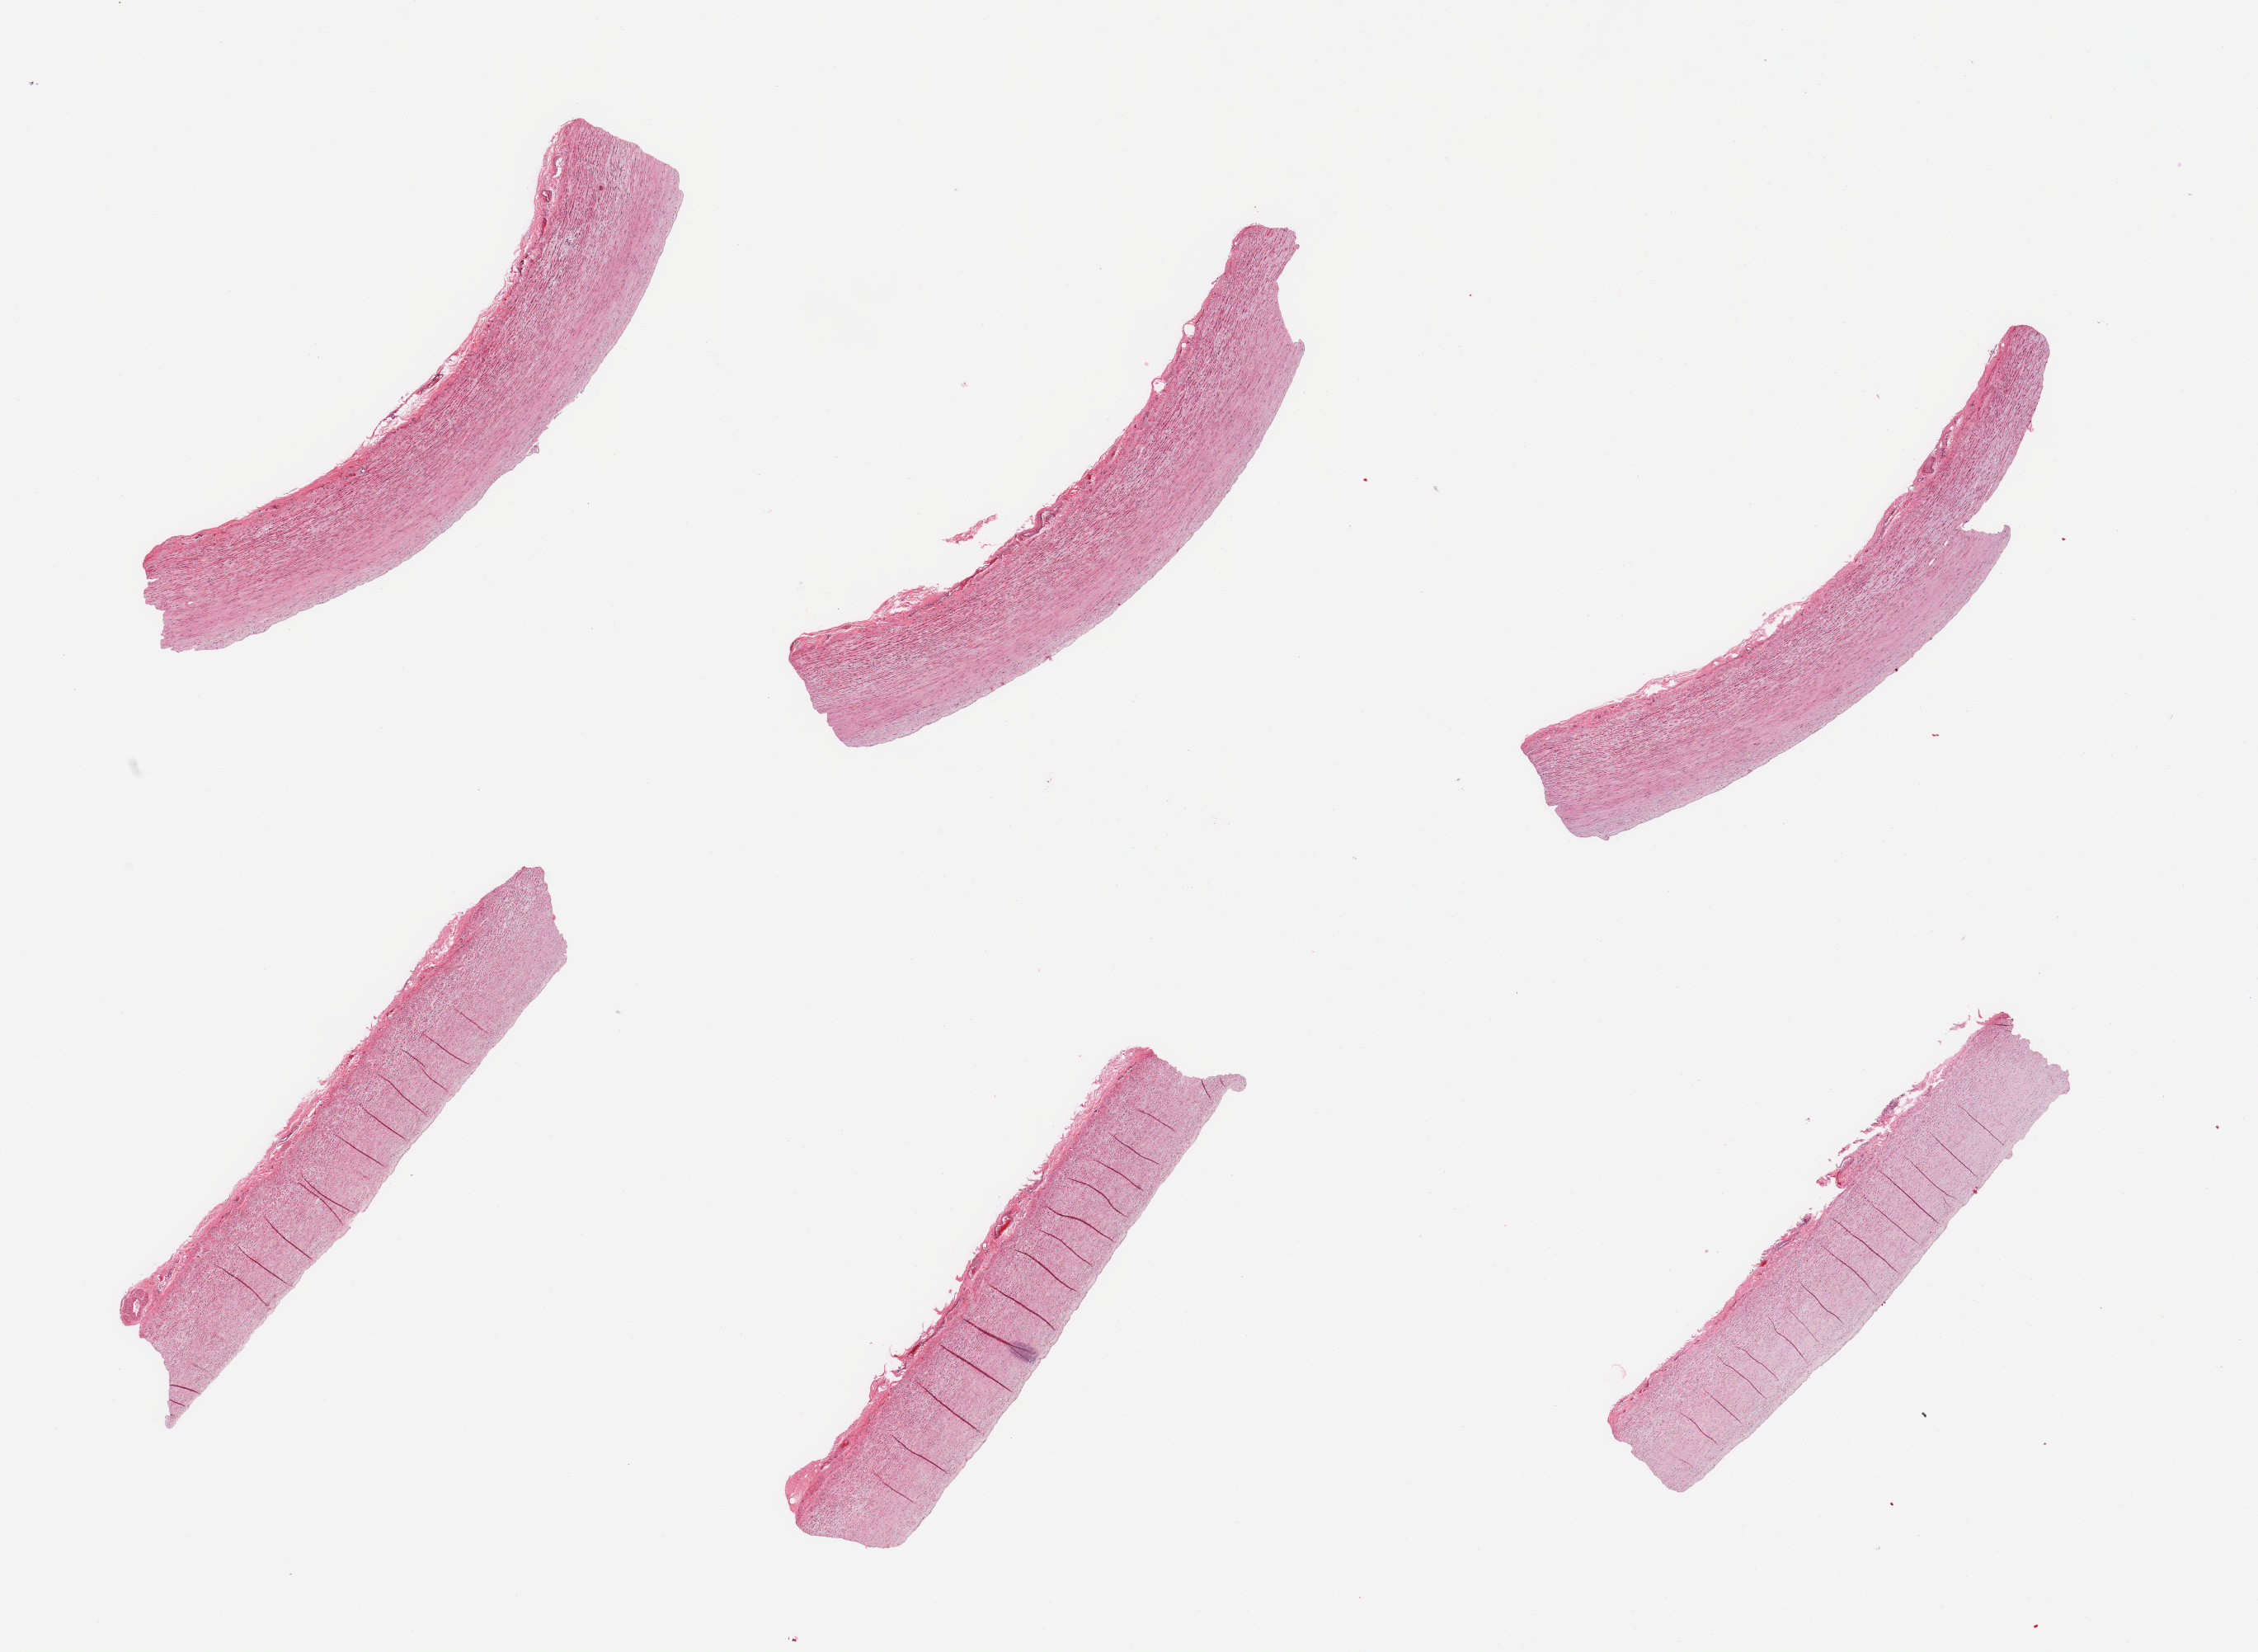
Whole-slide image, haematoxylin and eosin stain, brightfield — whole scanned area (about 21.7 x 15.8 mm, from a 20x scan) shown as a low-resolution overview; PAXgene-fixed paraffin-embedded (PFPE) section; sampled site (target tissue): aorta; donor tissue sample. Donor sex: male.
Pathologist's review note for this sample: 6 pieces, no abnormalities.